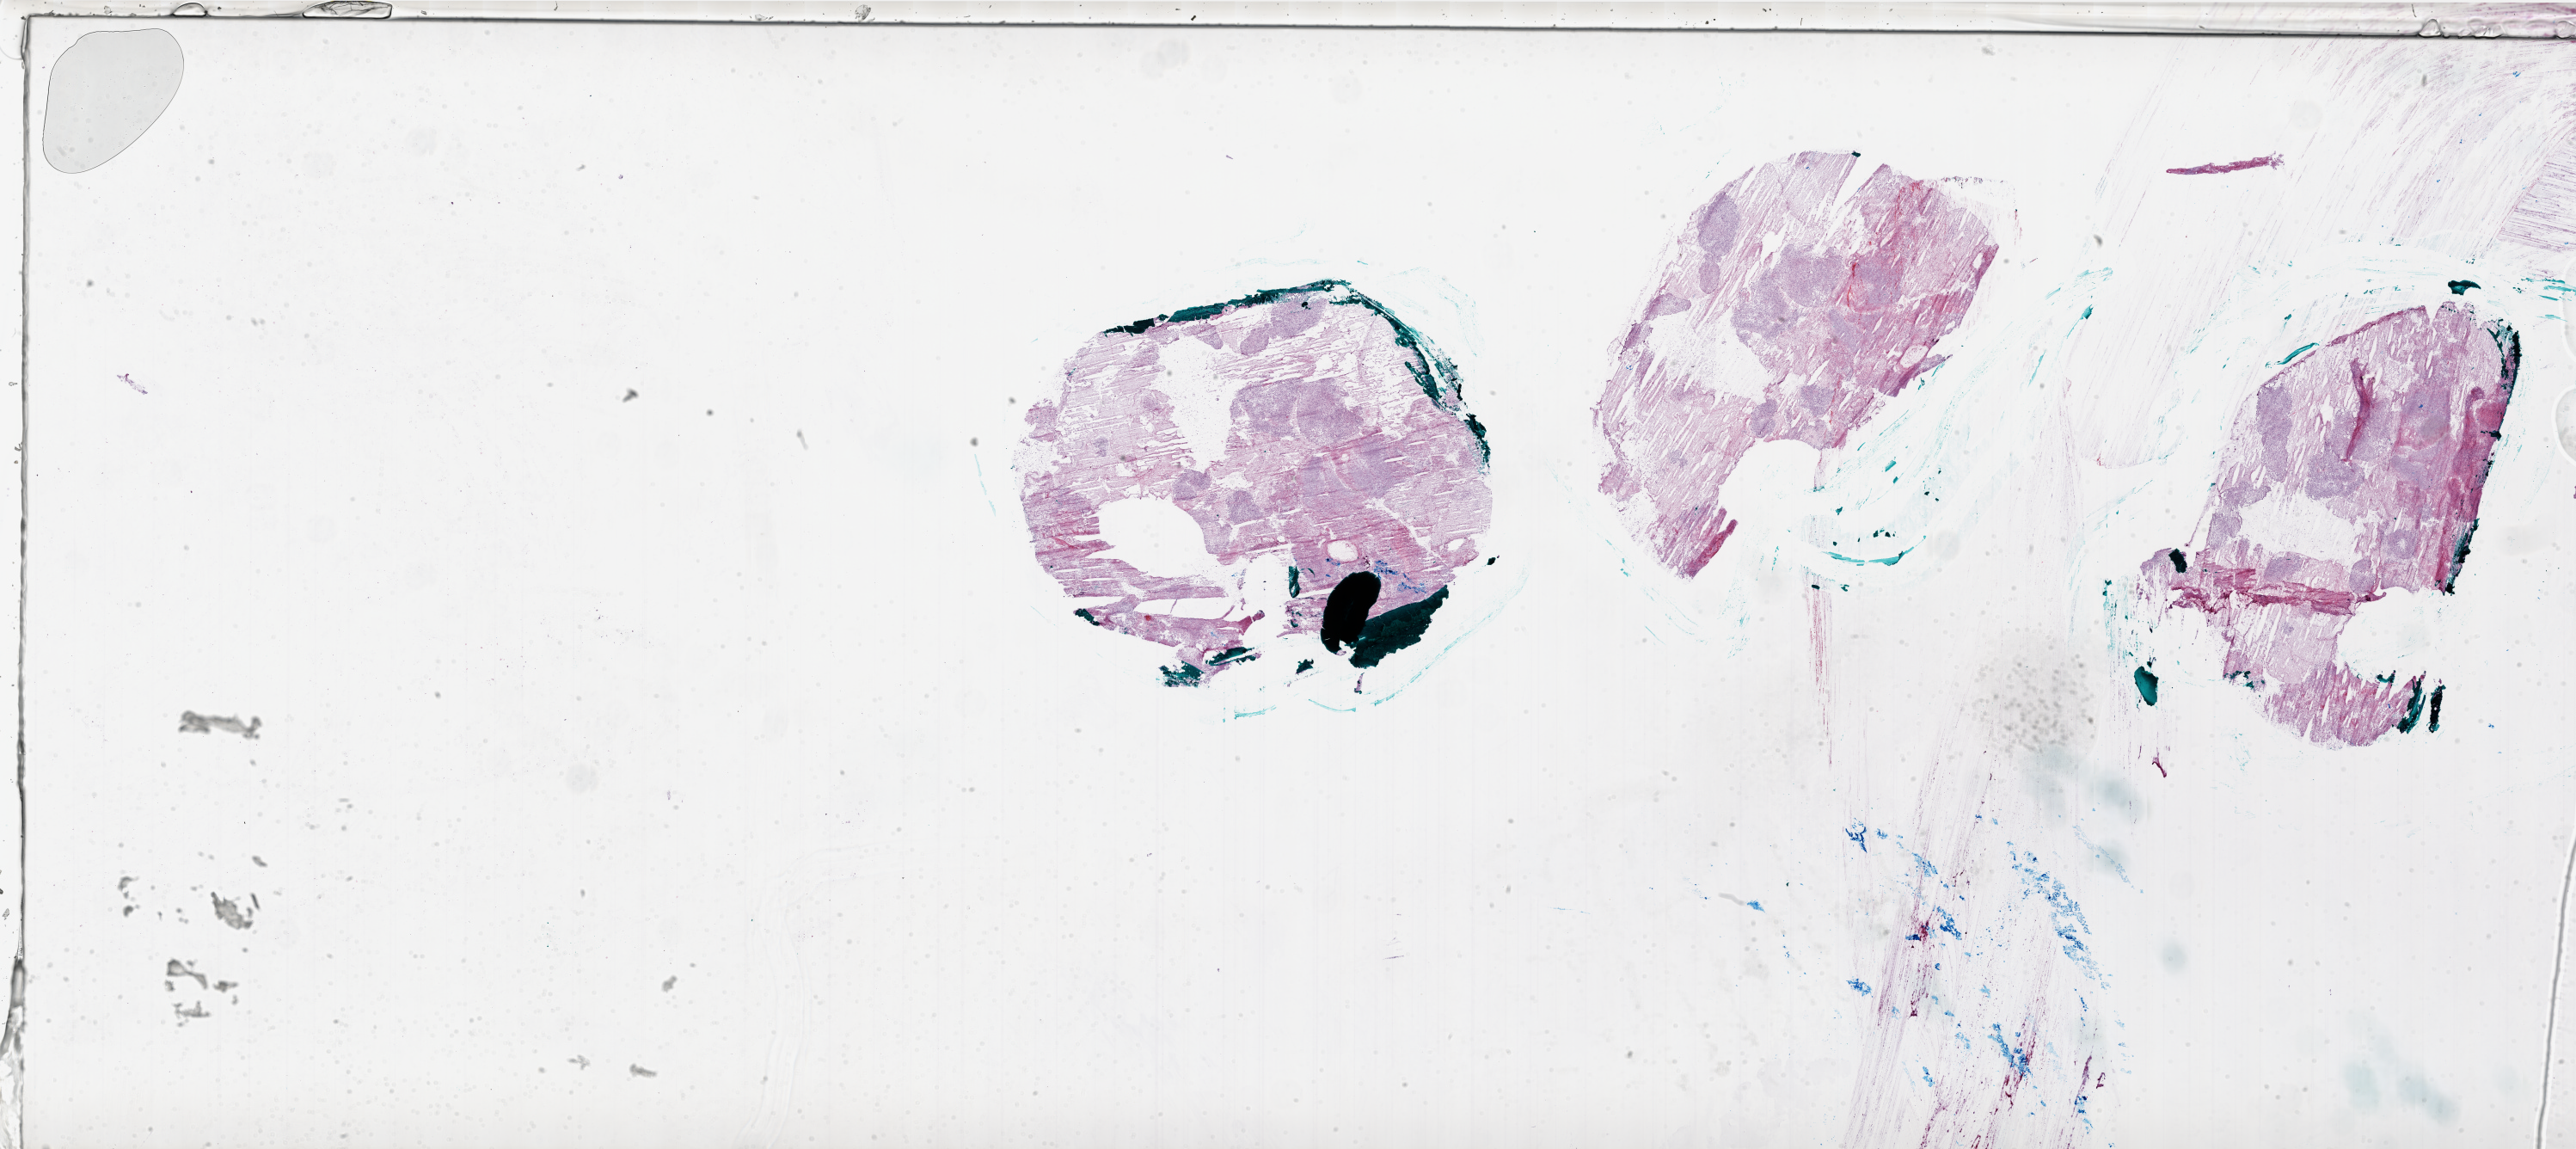
Digitized H&E-stained tissue section (whole slide) — shown as a low-resolution overview of the whole scanned area (about 48.0 x 21.4 mm, slide scanned at 20x), frozen section from the bottom of the tissue portion, sample: primary tumour, brain. Female patient; age at initial diagnosis 72 years.
Diagnosis: Glioblastoma.